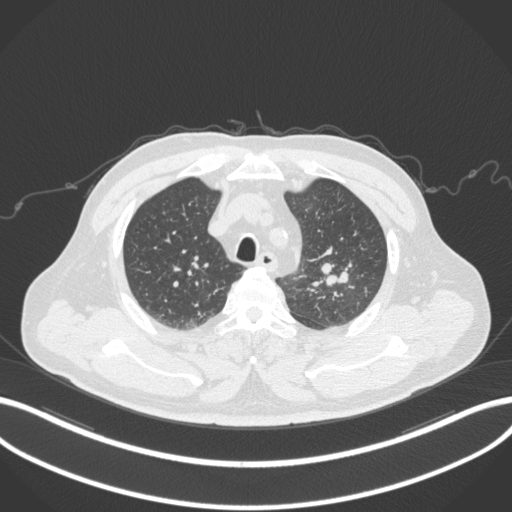
Chest CT, one axial slice; lung window (W 1500 / L -600 HU); 1 mm slice thickness; 512 × 512 image matrix, field of view 400 × 400 mm. Male patient, age 67 years. Case-level facts recorded for this patient, not image findings: clinical TNM (as recorded): T2a N1 M0.
Structures marked on this image (rectangle marked by the reading radiologist):
- lung tumour (recorded histology: adenocarcinoma): box from (x=318, y=261) to (x=355, y=288) px